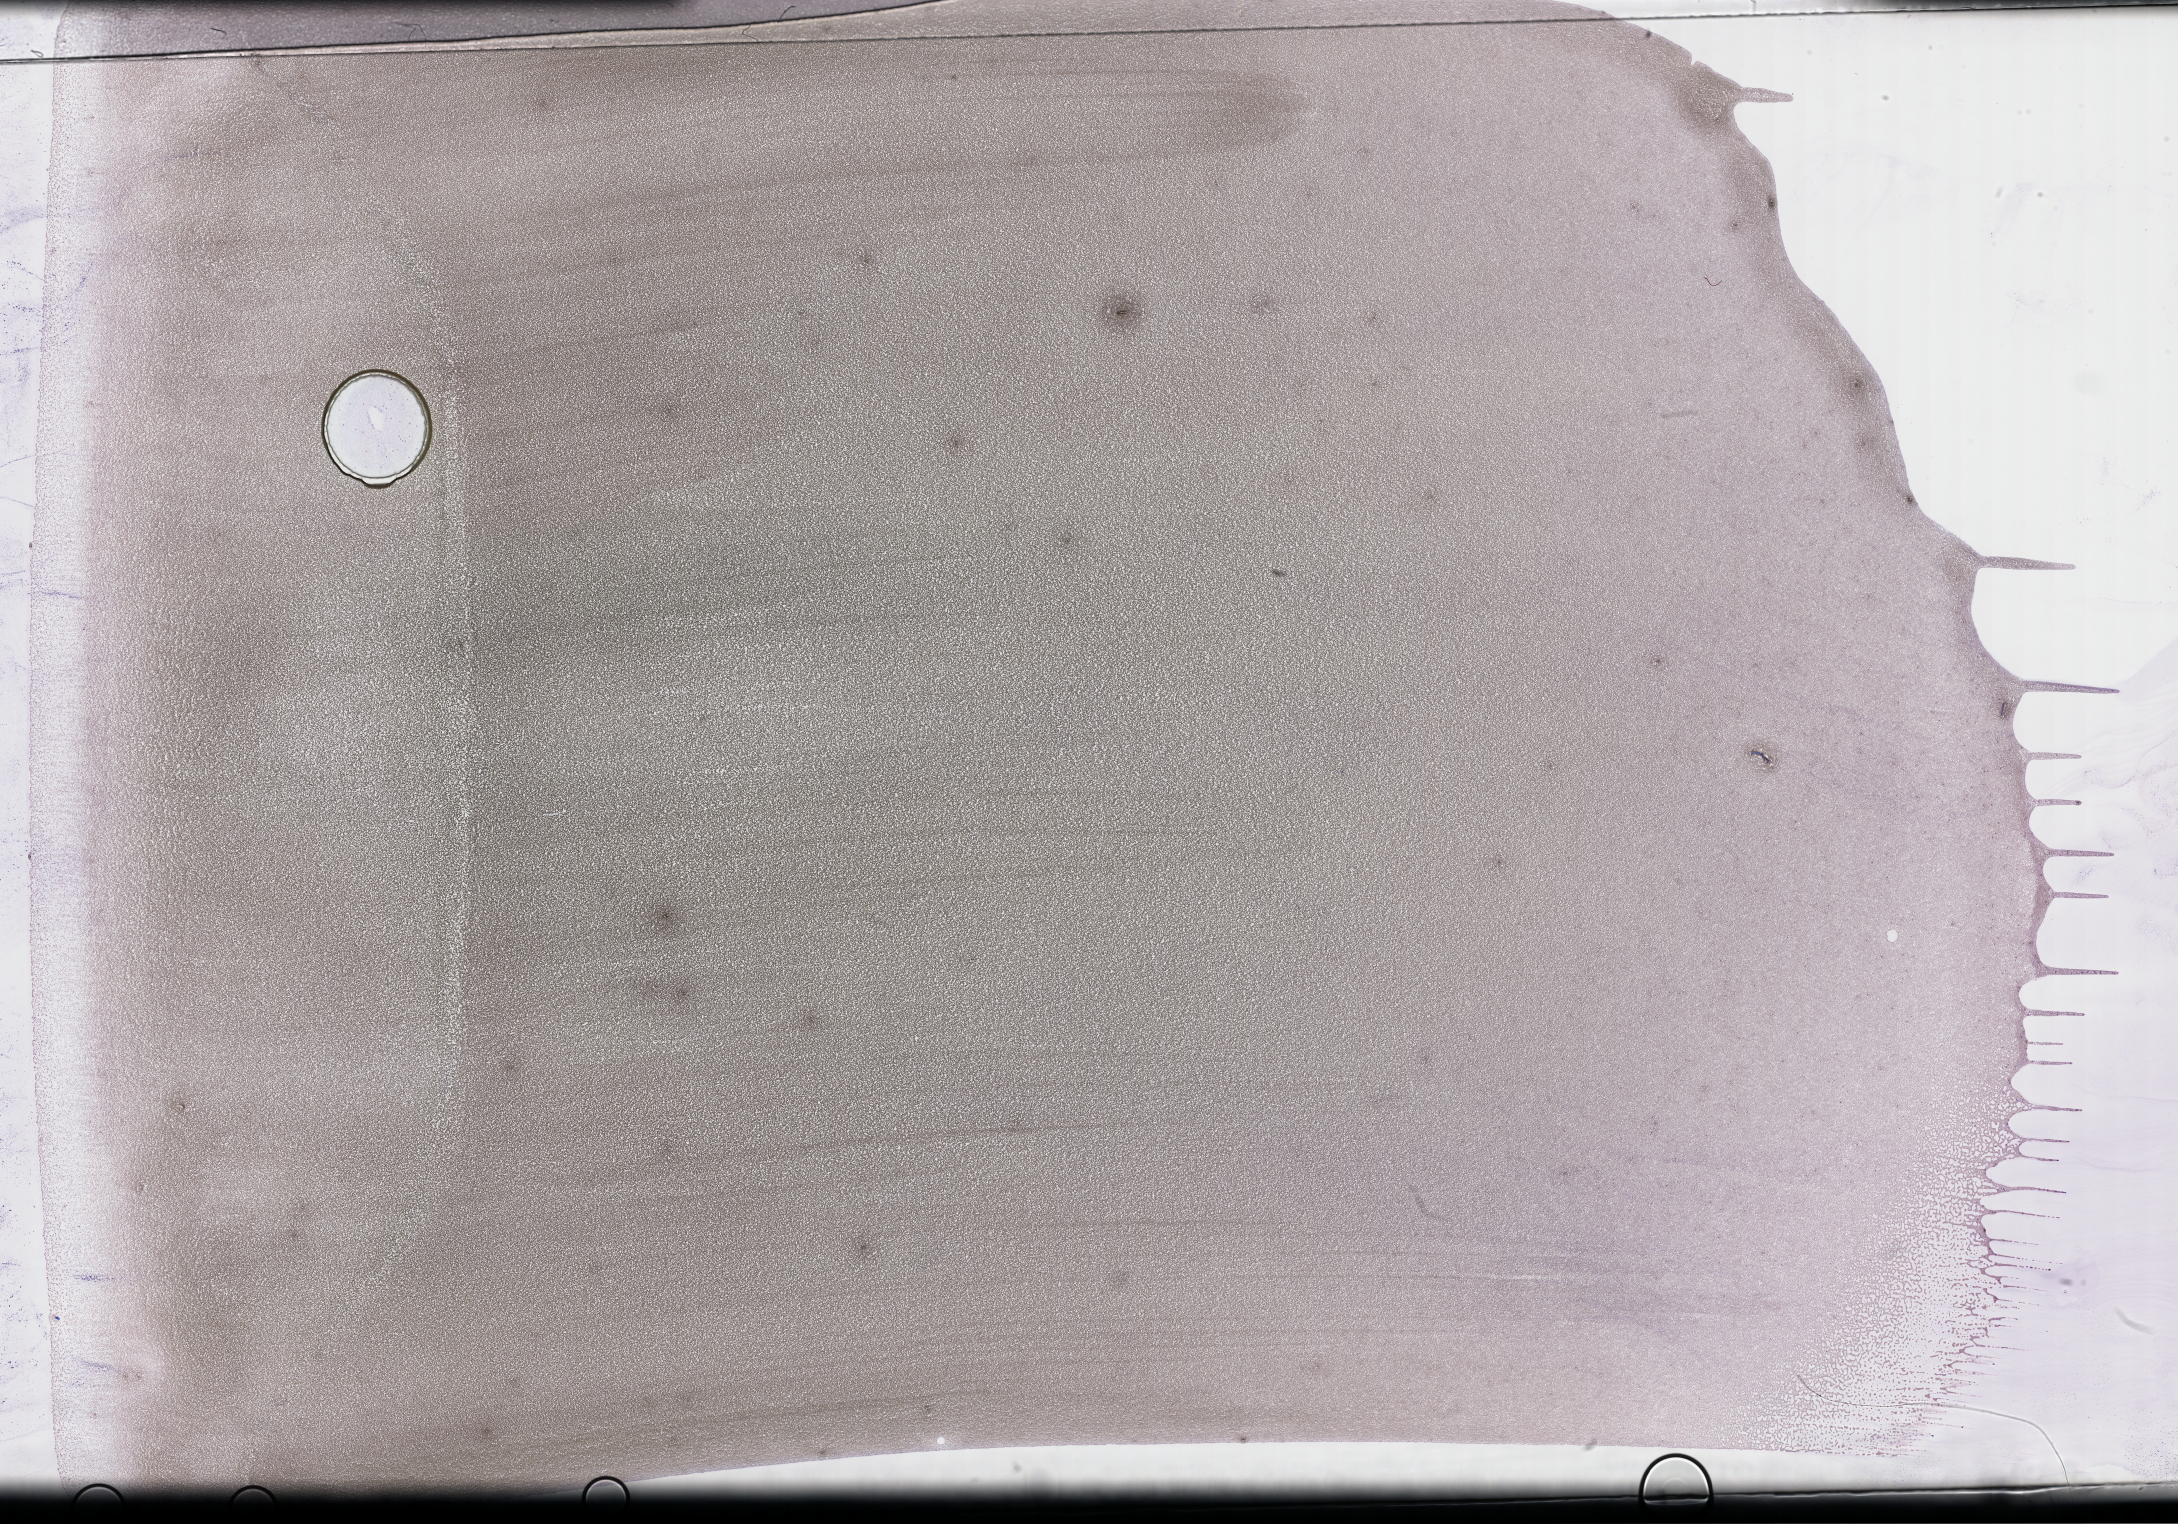
Whole-slide image of a whole blood smear, Wright-Giemsa stain — a low-resolution overview of the entire scanned area, about 35.2 x 24.6 mm. Patient sex: male.
Patient diagnosis: Plasma Cell Myeloma.